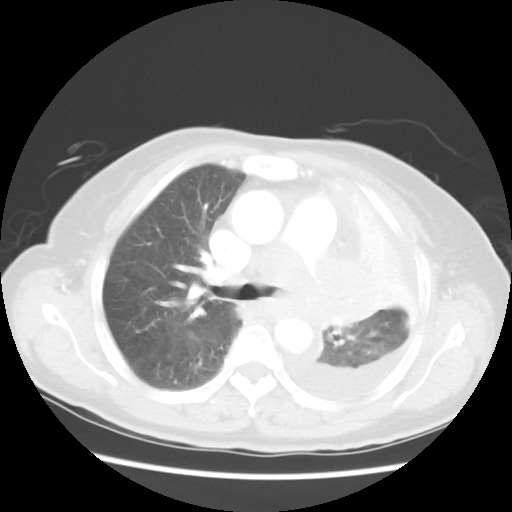
Chest CT, one axial slice; position 35 of 52 along the scan axis; reconstruction kernel STANDARD; 120 kVp; lung window (W 1500 / L -600 HU); 5 mm slice thickness; 512 × 512 image matrix, field of view 336 × 336 mm. Patient: female, 72 years. Case-level facts recorded for this patient, not image findings: clinical TNM (as recorded): T4 N3 M1b; histopathological grade: G3.
Outlined on this slice (bounding box drawn by a radiologist):
- lung tumour (recorded histology: large cell carcinoma): box from (x=287, y=244) to (x=392, y=345) px